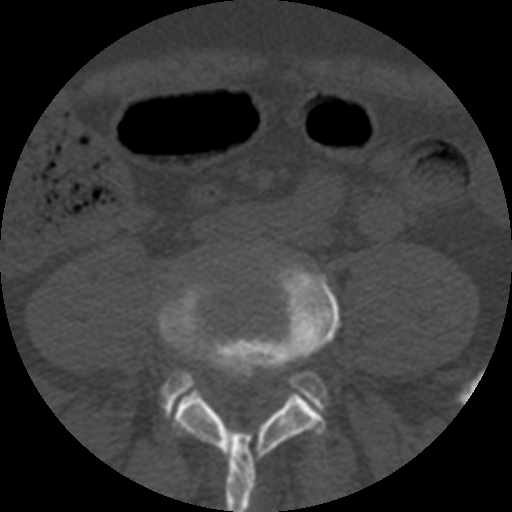
CT including the spine, one axial slice. Position 81 of 508 along the scan axis. Reconstruction kernel STANDARD. 120 kVp. Bone window (W 1800 / L 400 HU). 512 × 512 image matrix, field of view 160 × 160 mm. Patient age 57 years. From the clinical record (not read from this slice): primary cancer: prostate.
Annotated regions visible in this slice (semi-automatically segmented with operator editing):
- L4 vertebra: bounding box [x1, y1, x2, y2] px = [157, 260, 340, 512]
- L5 vertebra: [162, 371, 328, 416]